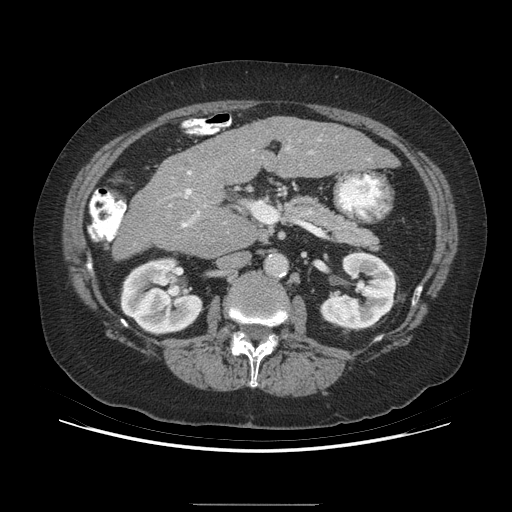
Contrast-enhanced abdominal CT (liver protocol), one axial slice; slice 142 of 192 in the series (ordered by position); 140 kVp; soft-tissue window (W 400 / L 40 HU); 512 × 512 image matrix, field of view 400 × 400 mm. From the clinical record (not read from this slice): diagnosis: hepatocellular carcinoma (patient treated with transarterial chemoembolisation; whether this scan precedes or follows treatment is not stated here); TNM stage (as recorded): Stage-I.
Structures marked on this image (semi-automatic segmentation, software-assisted and operator-edited):
- liver parenchyma outside the tumour (the mass and vessels are separate outlines, so this box may not span the whole liver): box from (x=112, y=116) to (x=396, y=258) px
- liver vessels: (x=169, y=189)–(x=200, y=227)